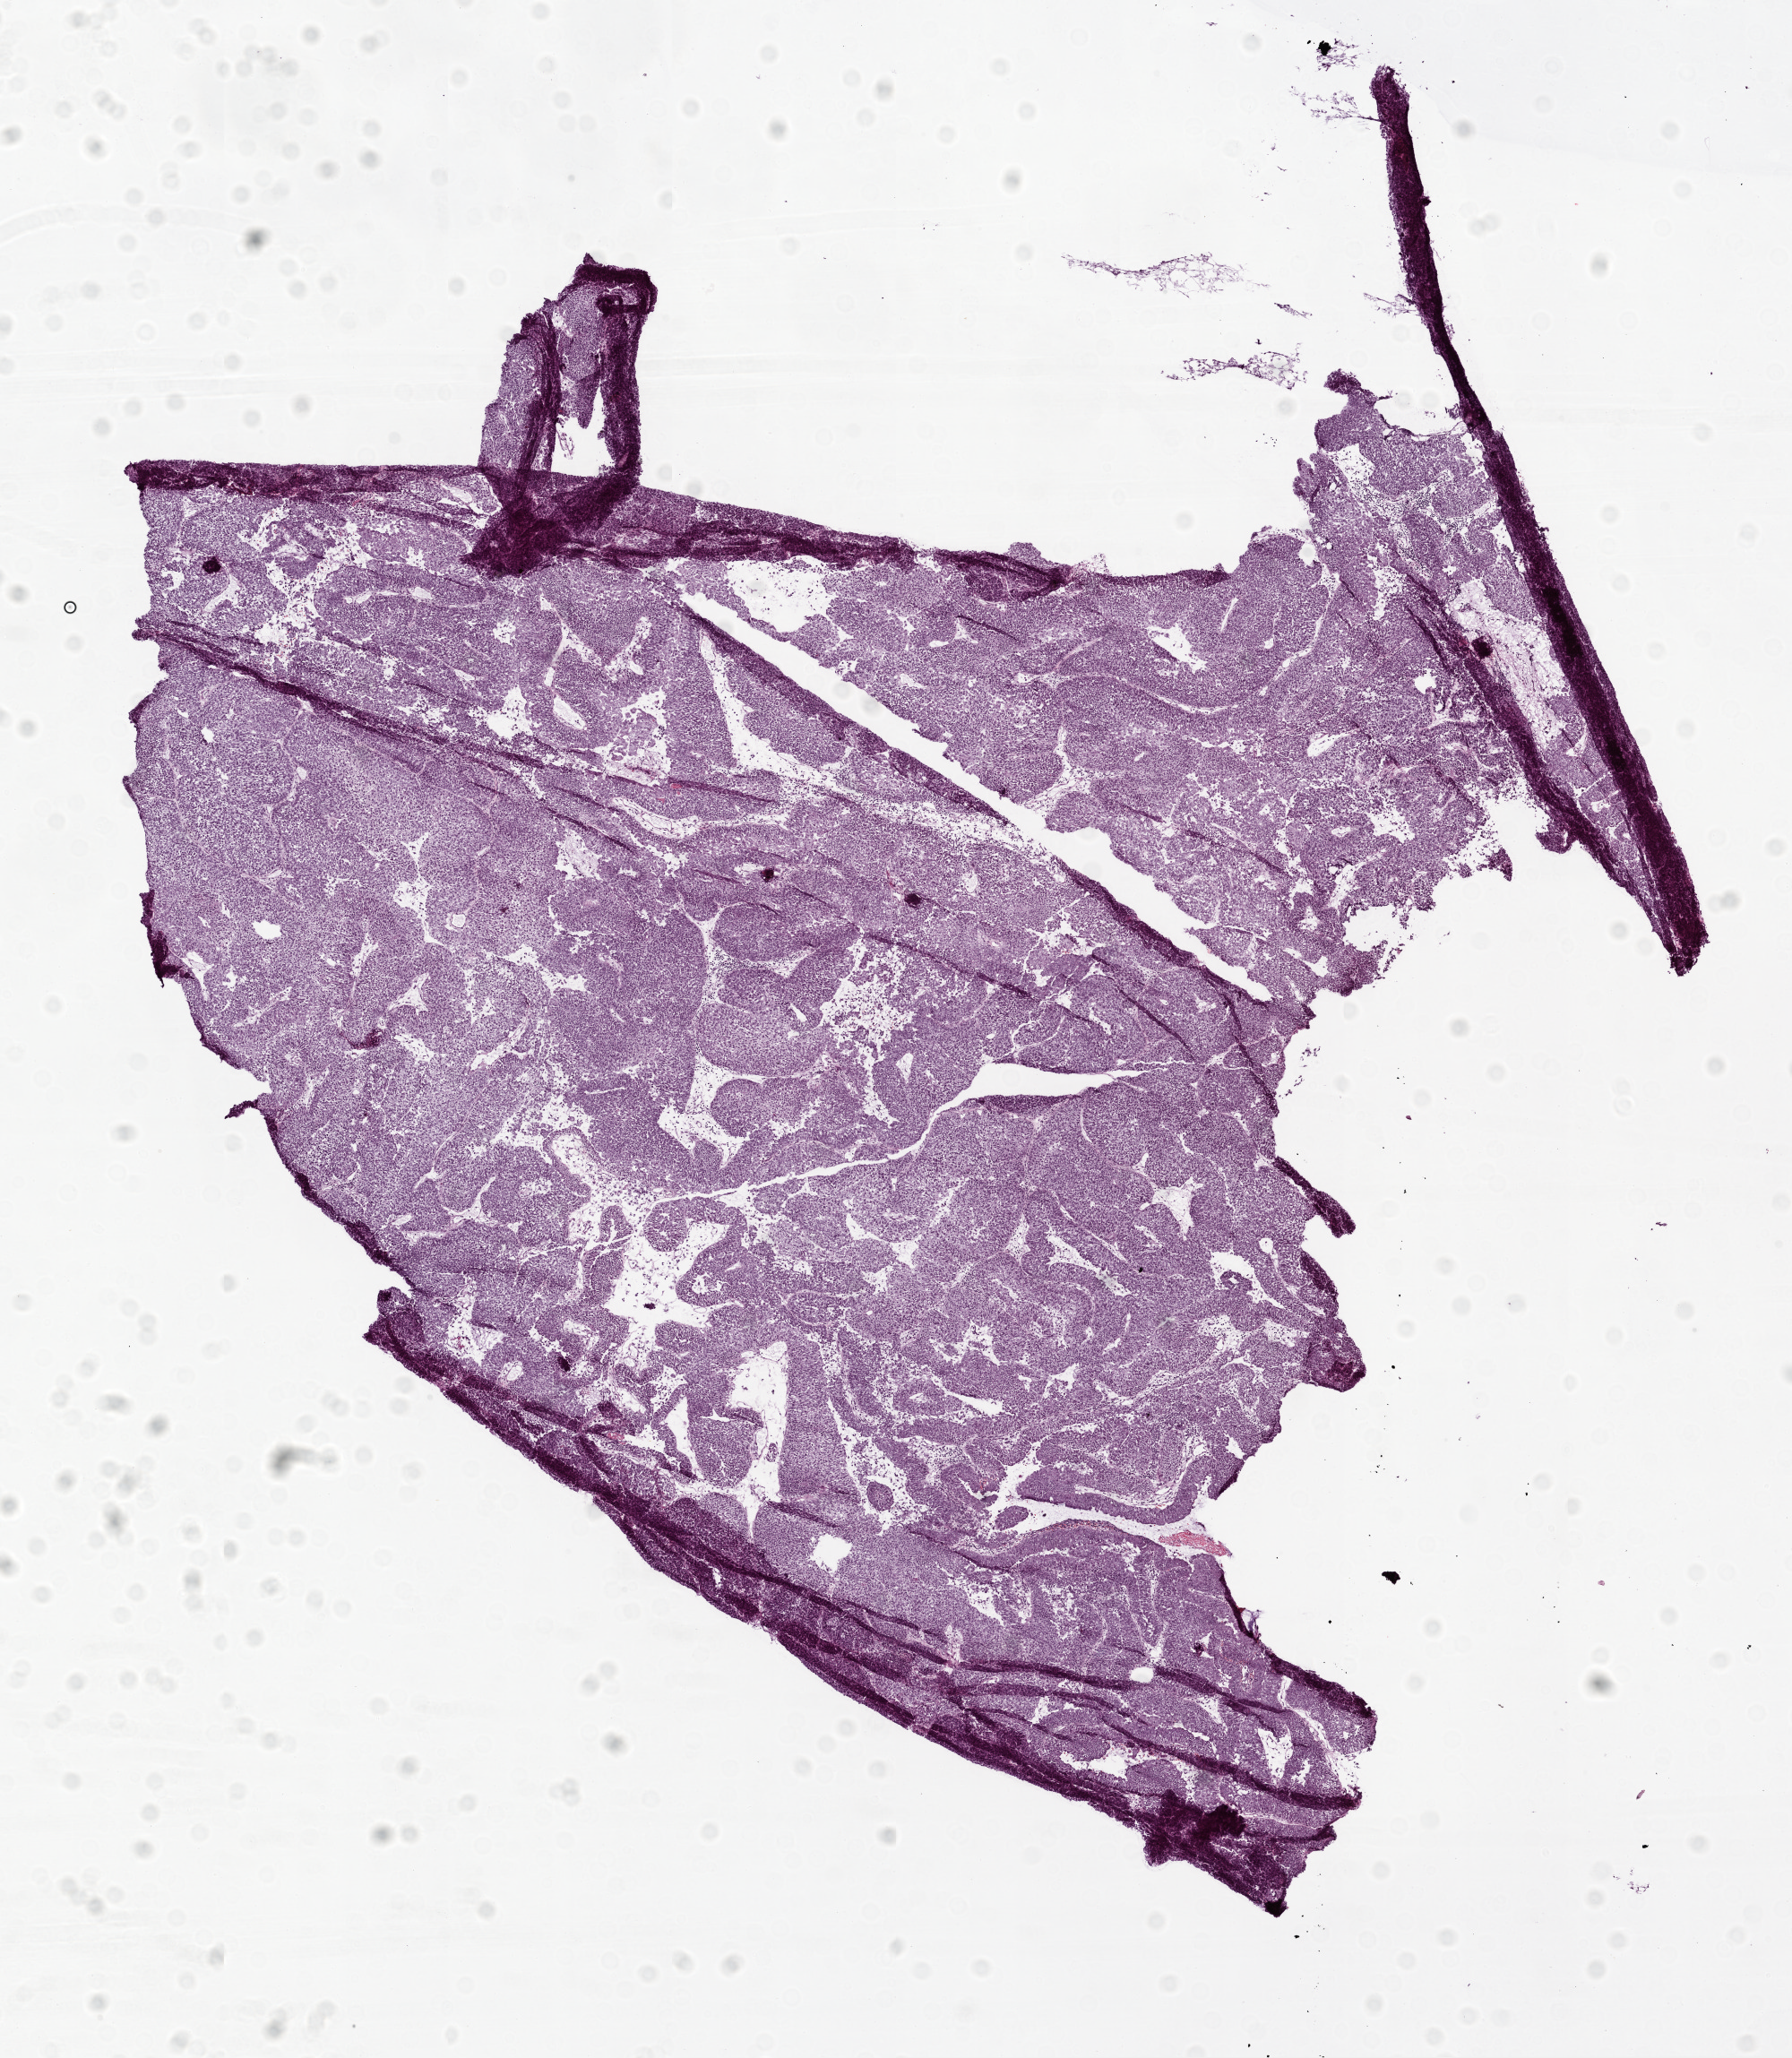
Digitized H&E-stained tissue section (whole slide), whole scanned area (about 8.0 x 9.2 mm, acquisition: 20x scan) shown as a low-resolution overview; frozen section; ovary, primary tumour sample. Female, age 71 years at initial diagnosis. Histologic grade: G3 (poorly differentiated). Slide review estimates, as recorded: tumour cells 95%, tumour nuclei 95%, normal cells 1%, stromal cells 4%, necrosis 0%.
• FIGO stage: IA
• diagnosis: Serous cystadenocarcinoma, NOS